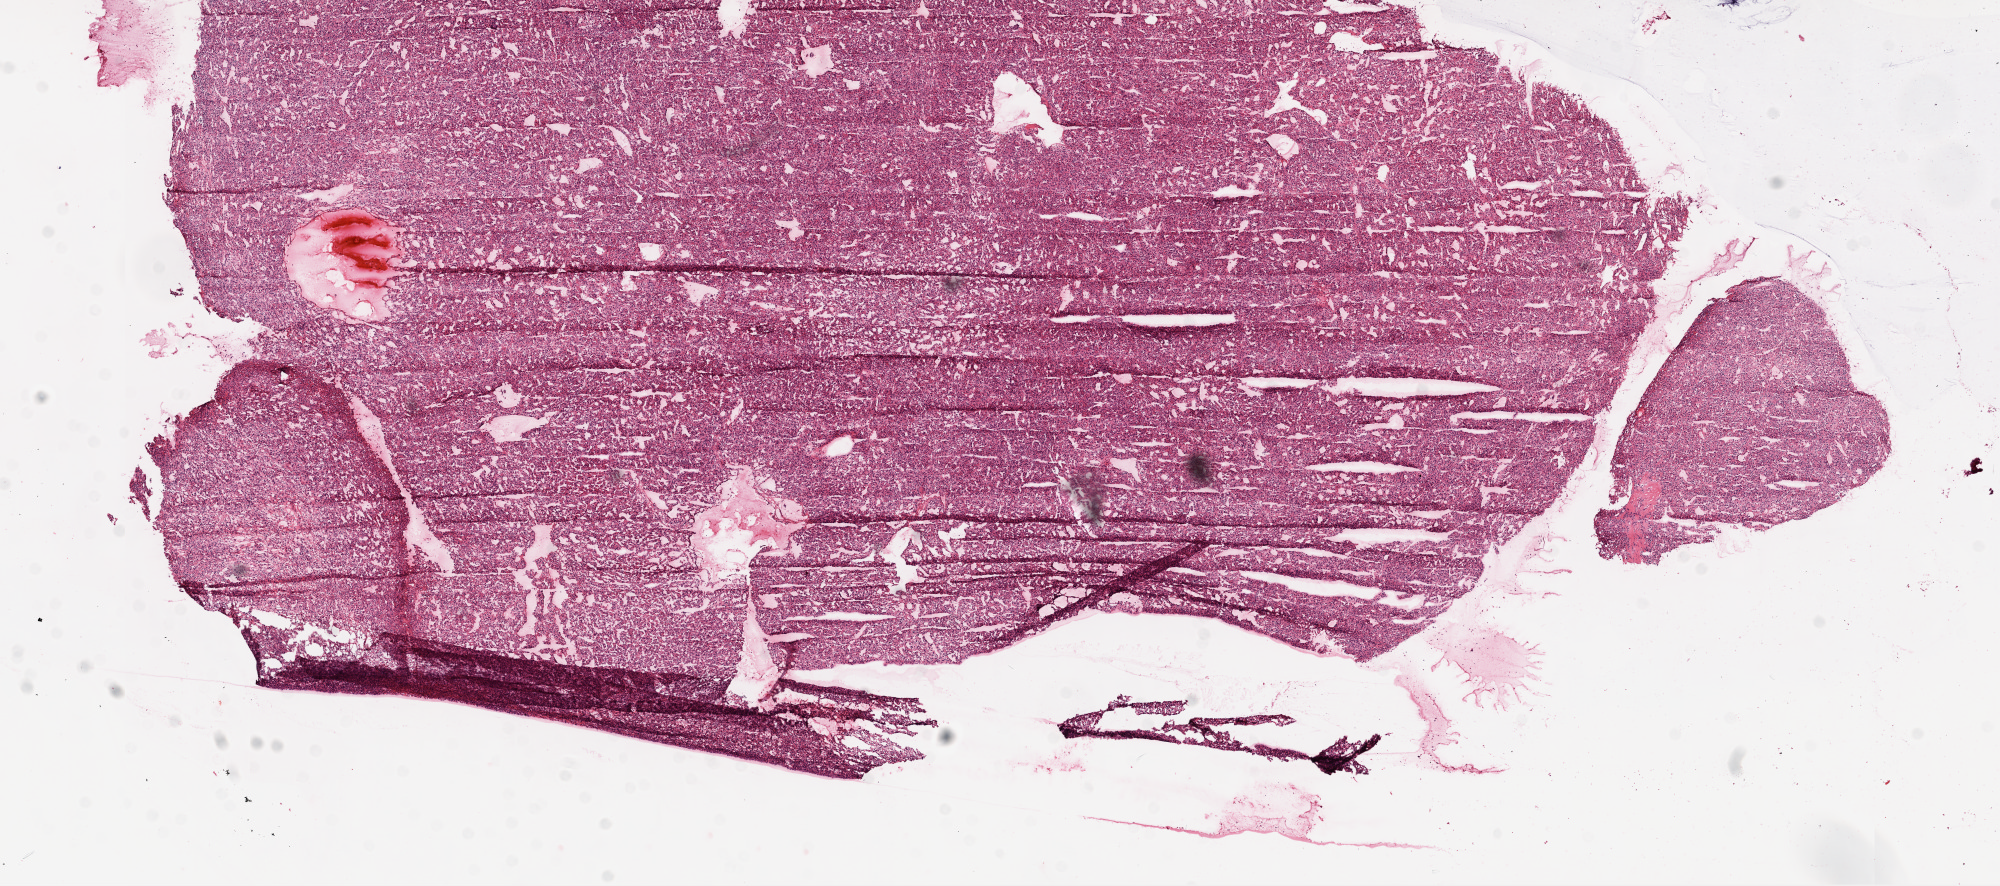
Digitized H&E tissue section (whole slide) — a low-resolution overview of the entire scanned area, about 16.0 x 7.1 mm; frozen section from the top of the tissue portion; sample: primary tumour, kidney. Patient: male, age at initial diagnosis 70 years. Histologic grade: G2 (moderately differentiated). Composition of this section per pathologist review: tumour cells 95%, tumour nuclei 90%, normal cells 0%, stromal cells 5%, necrosis 0%.
Laterality: right. AJCC pathologic stage: IV (6th edition). Diagnosis: Clear cell adenocarcinoma, NOS.